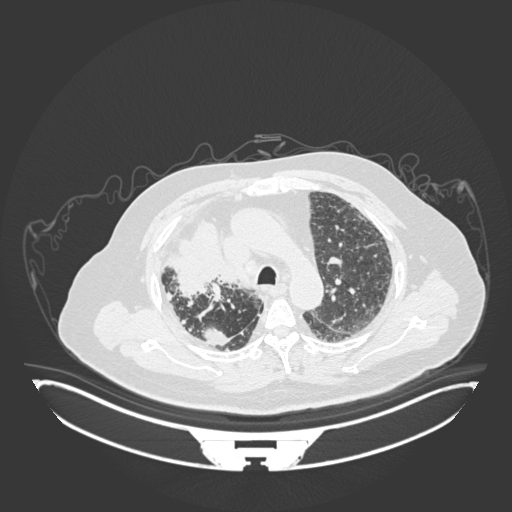
Chest CT, one axial slice. 120 kVp. Lung window (W 1500 / L -600 HU). 1 mm slice thickness. 512 × 512 image matrix. Male patient, age 69 years. From the clinical record (not read from this slice): clinical TNM (as recorded): T4 N3 M1.
Structures marked on this image (rectangle marked by the reading radiologist):
- lung tumour (recorded histology: adenocarcinoma): bounding box (x1, y1, x2, y2) in pixels: (164, 218, 226, 302)